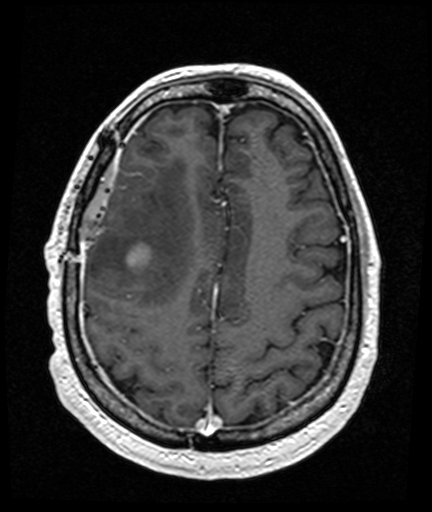
Brain MRI from a brain-tumour surgery series, one axial slice; position 48 of 176 along the scan axis; T1-weighted post-contrast; 1 mm slice thickness; 432 × 512 image matrix, field of view 194 × 230 mm. From the clinical record (not read from this slice): histopathology: Glioblastoma; WHO grade: 4; IDH mutation: no; tumour location: Right Frontal Temporal, Posterior Sylvian Fissure.
Outlined on this slice (manually delineated by an expert):
- tumour: box from (x=130, y=248) to (x=148, y=262) px